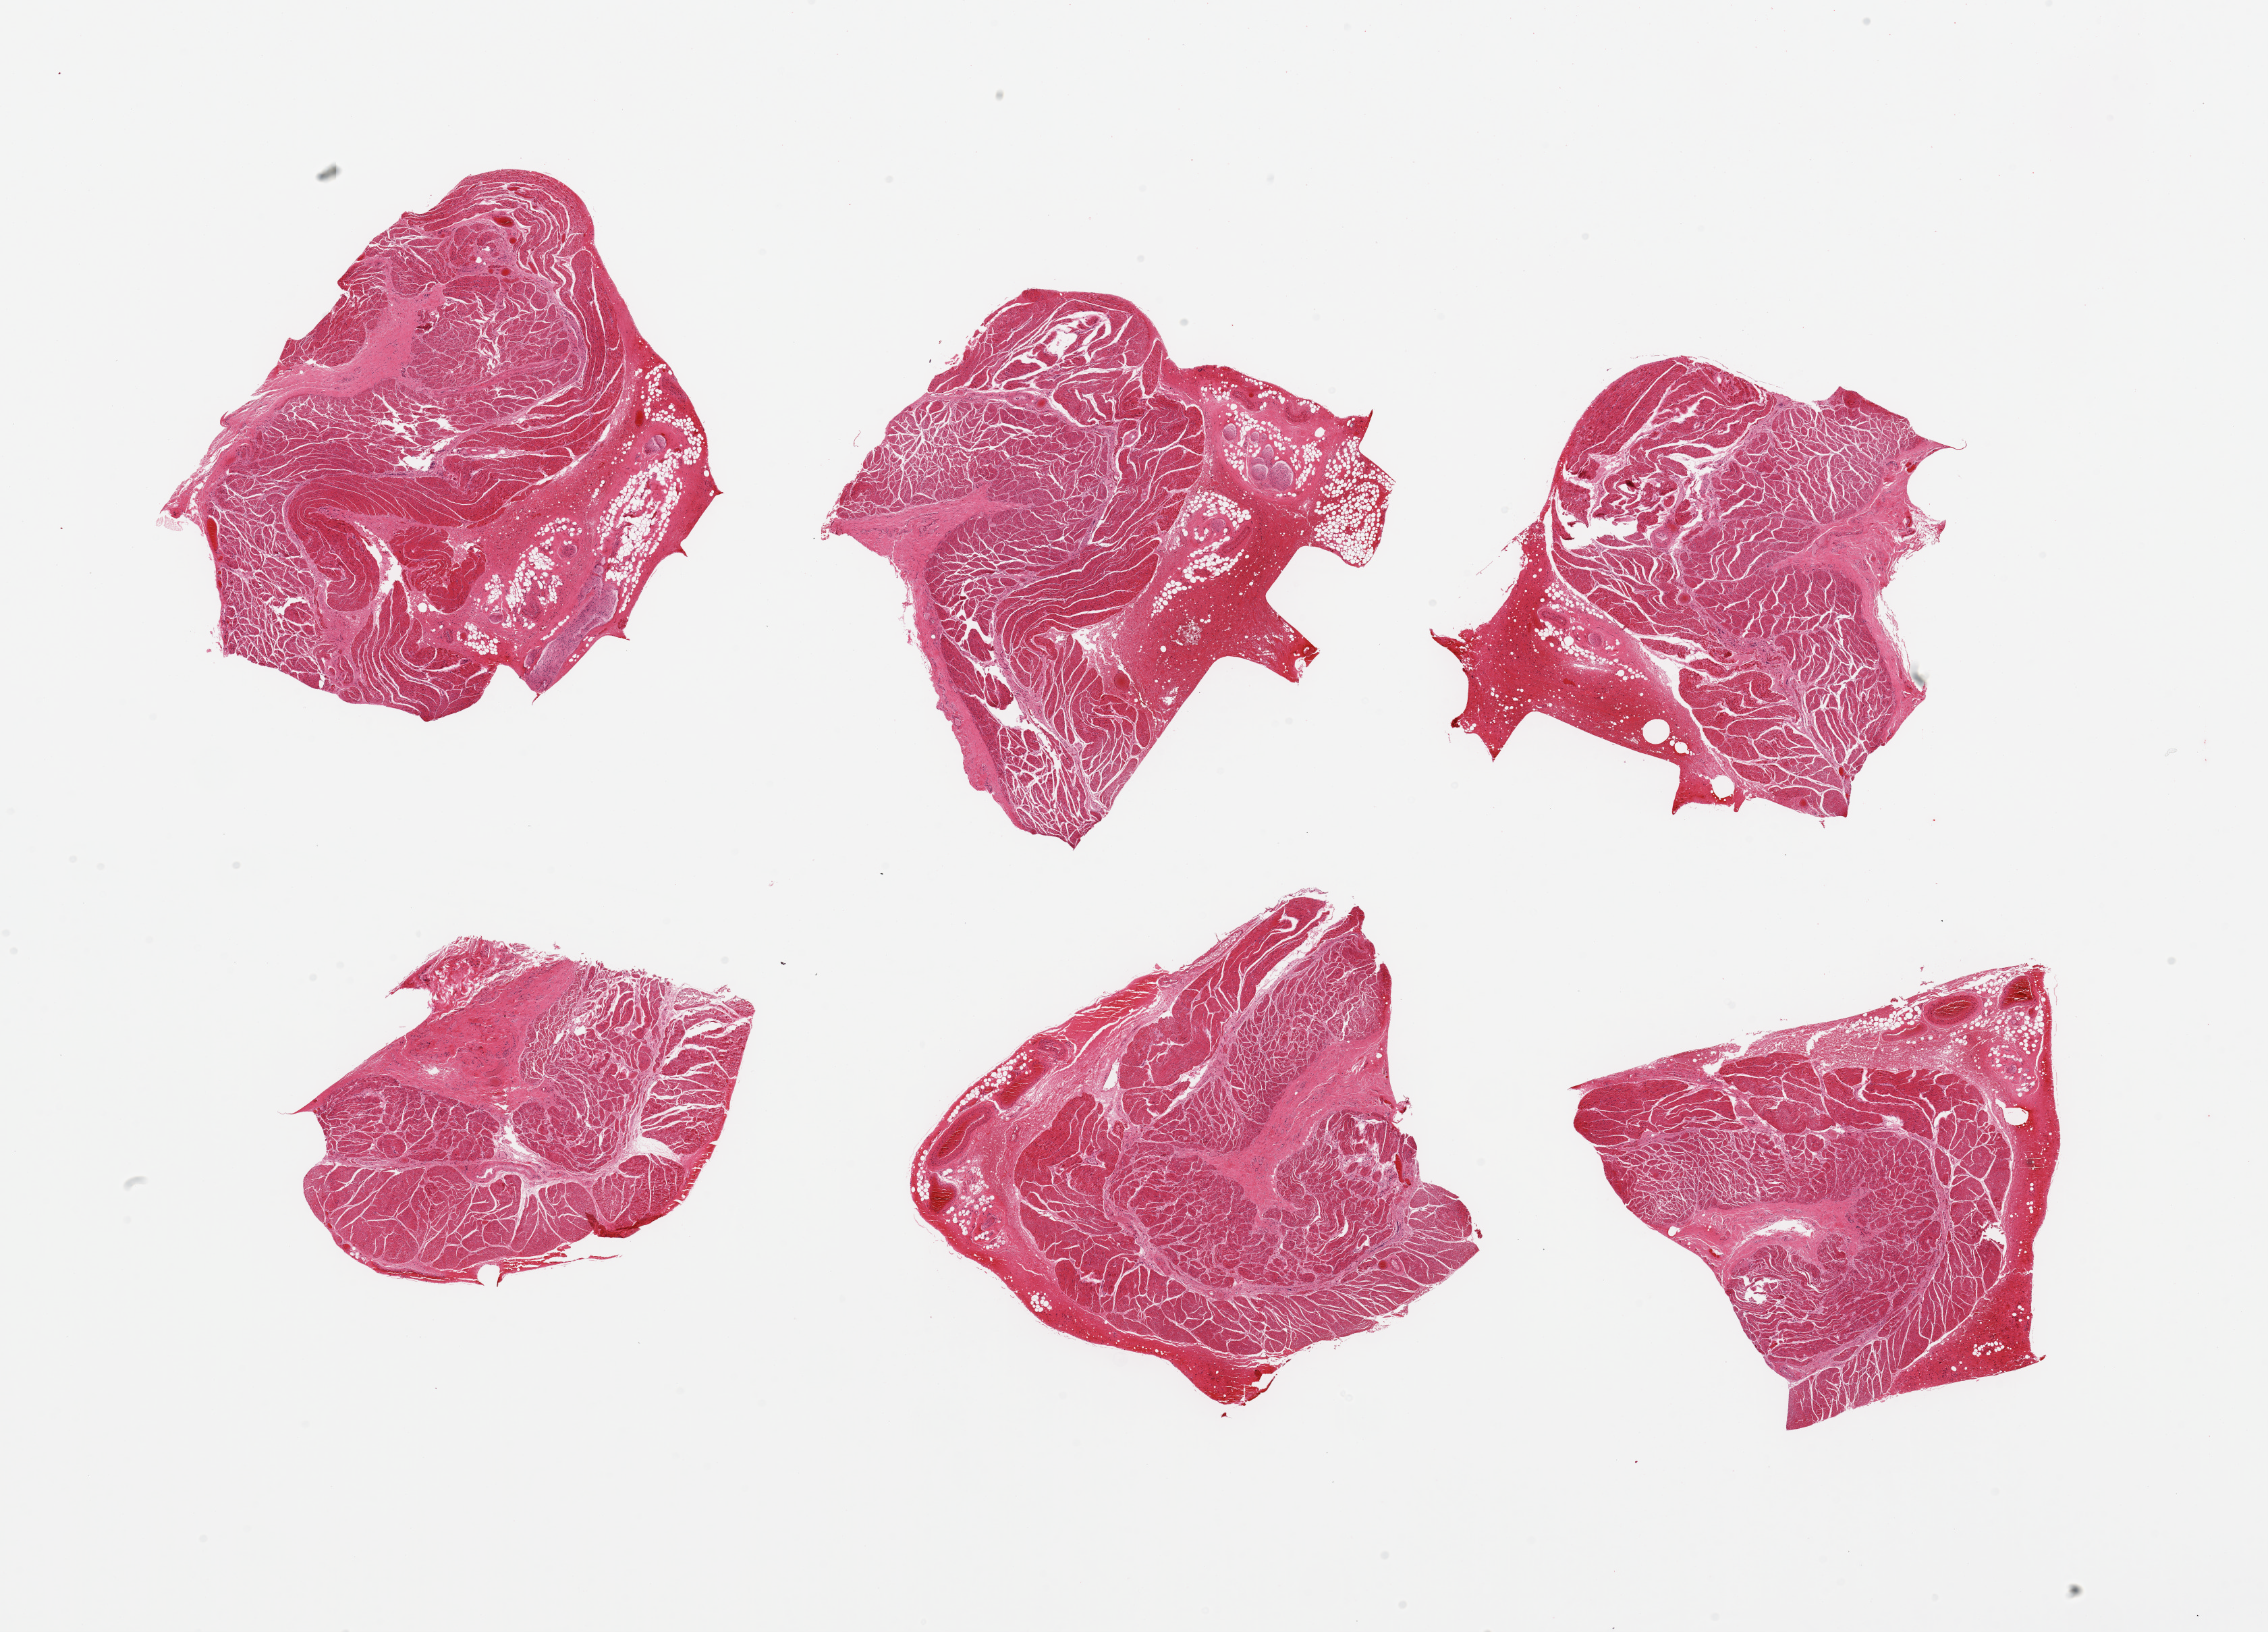
Whole-slide image, H&E stain, brightfield, shown as a low-resolution overview of the whole scanned area (about 26.6 x 19.1 mm, acquisition: 20x scan). PAXgene-fixed paraffin-embedded (PFPE) section. Sampled site (target tissue): esophageal muscle. Donor tissue sample. Donor: male.
Pathologist's review note for this sample: 6 pieces, target muscularis.